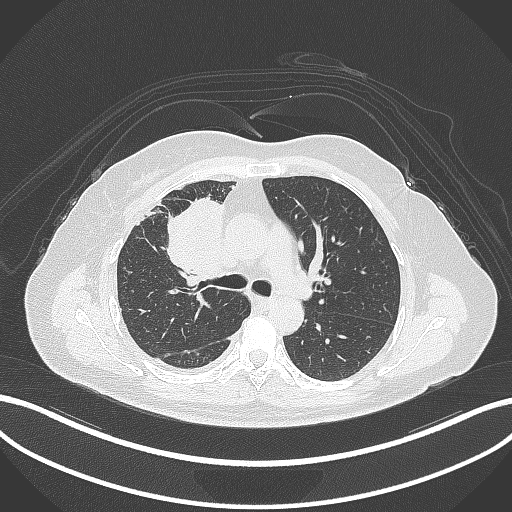
Chest CT, one axial slice; slice 180 of 305 in the series (ordered by position); lung window (W 1500 / L -600 HU); 1 mm slice thickness; 512 × 512 image matrix, field of view 400 × 400 mm. Patient: female, 52 years. From the clinical record (not read from this slice): clinical TNM (as recorded): T3 N1 M1.
Outlined on this slice (bounding box drawn by a radiologist):
- lung tumour (recorded histology: adenocarcinoma): bounding box <168,196,226,281> (left, top, right, bottom; pixels)